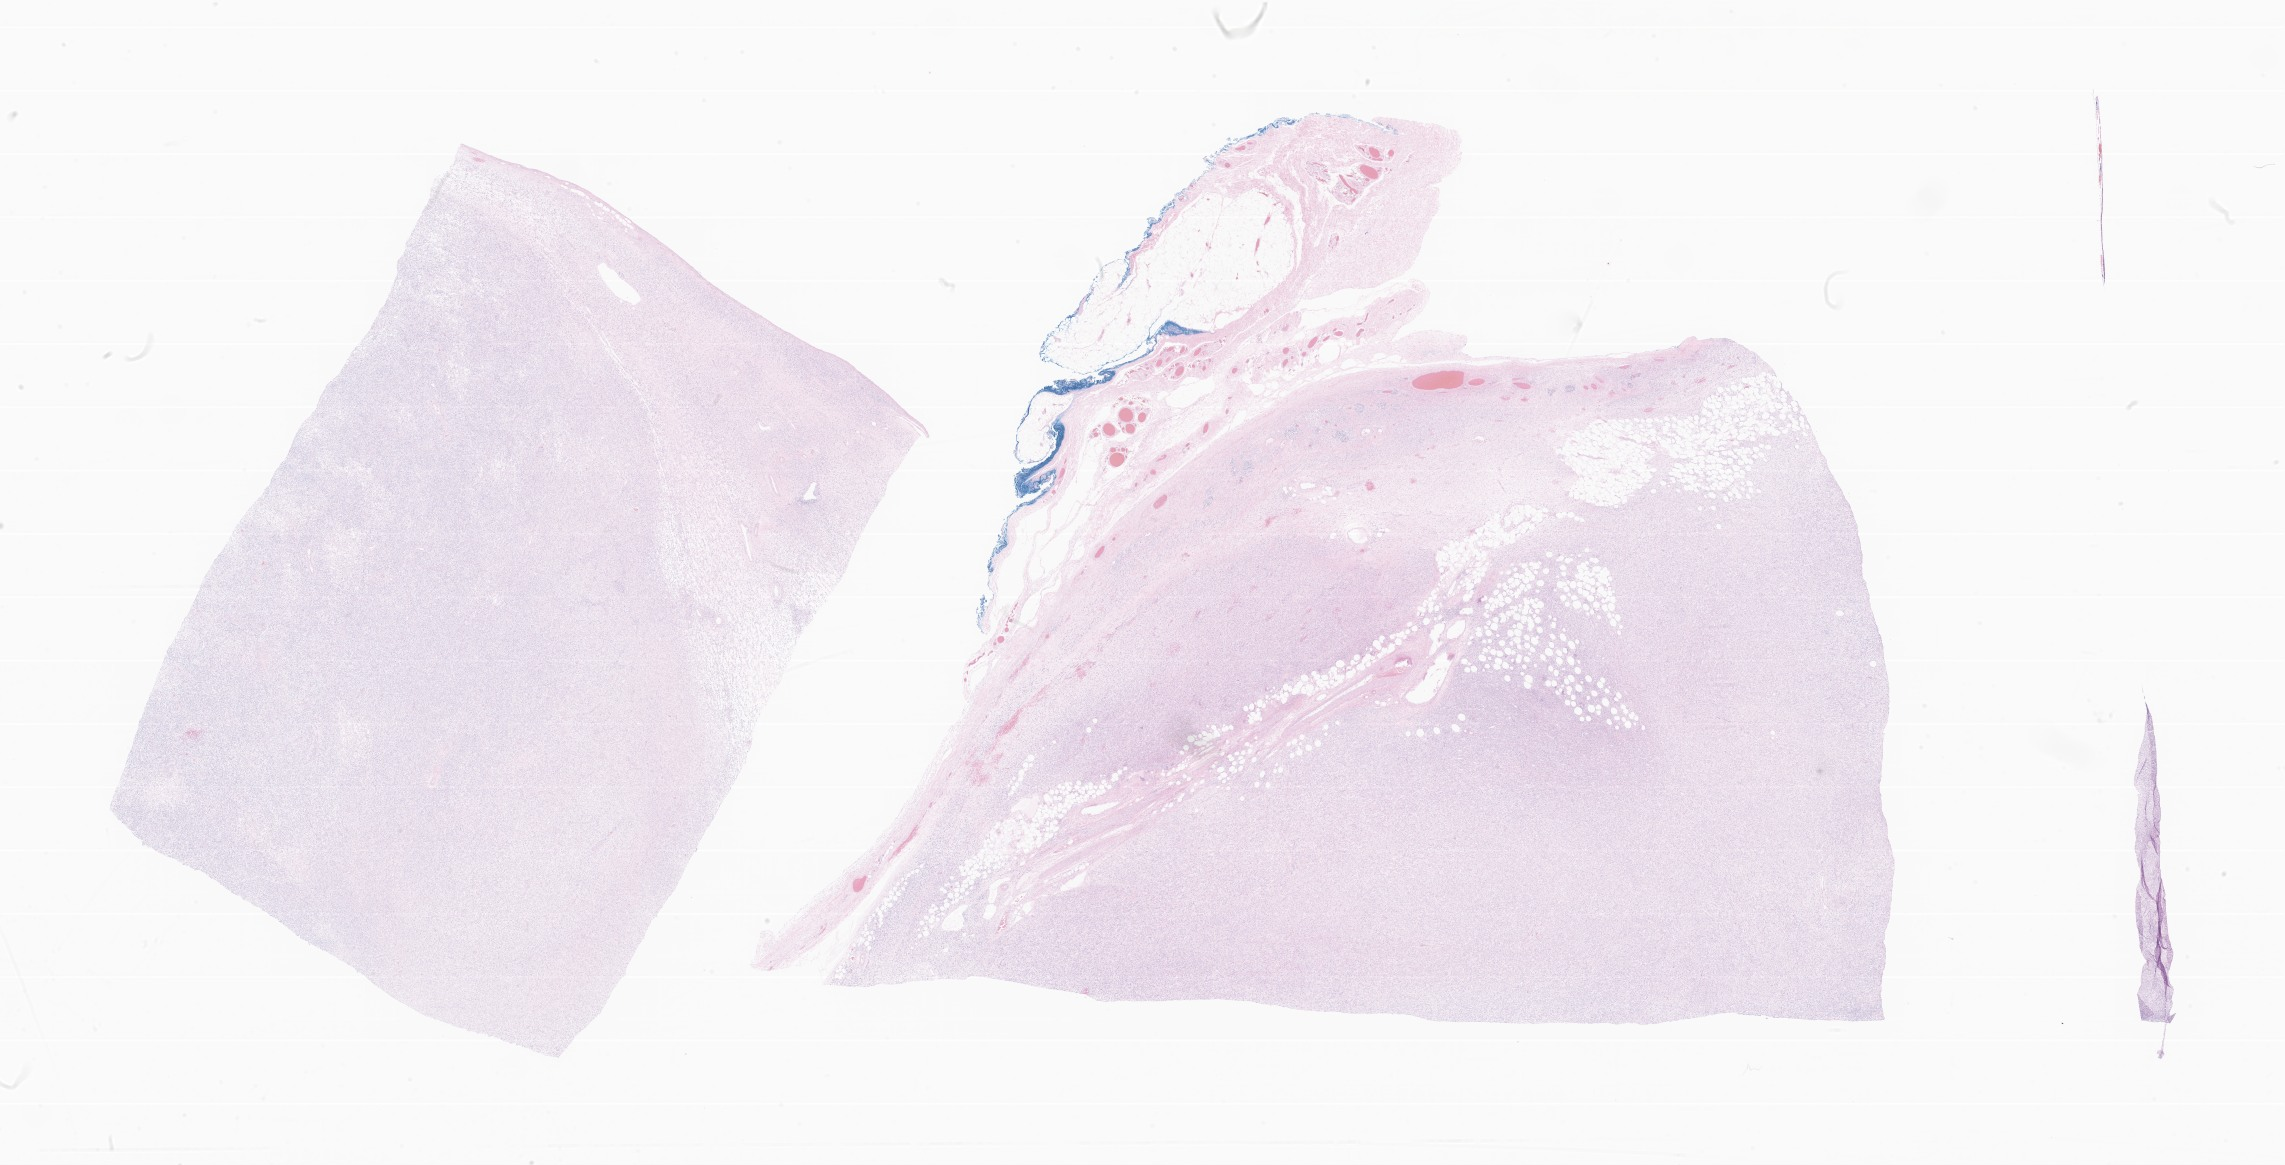
Whole-slide image, haematoxylin and eosin stain of tumor tissue from the testis, shown as a low-resolution overview of the whole scanned area (about 38.5 x 19.6 mm). FFPE section. Patient male; age 212 months.
Recorded diagnosis: Spindle cell rhabdomyosarcoma.